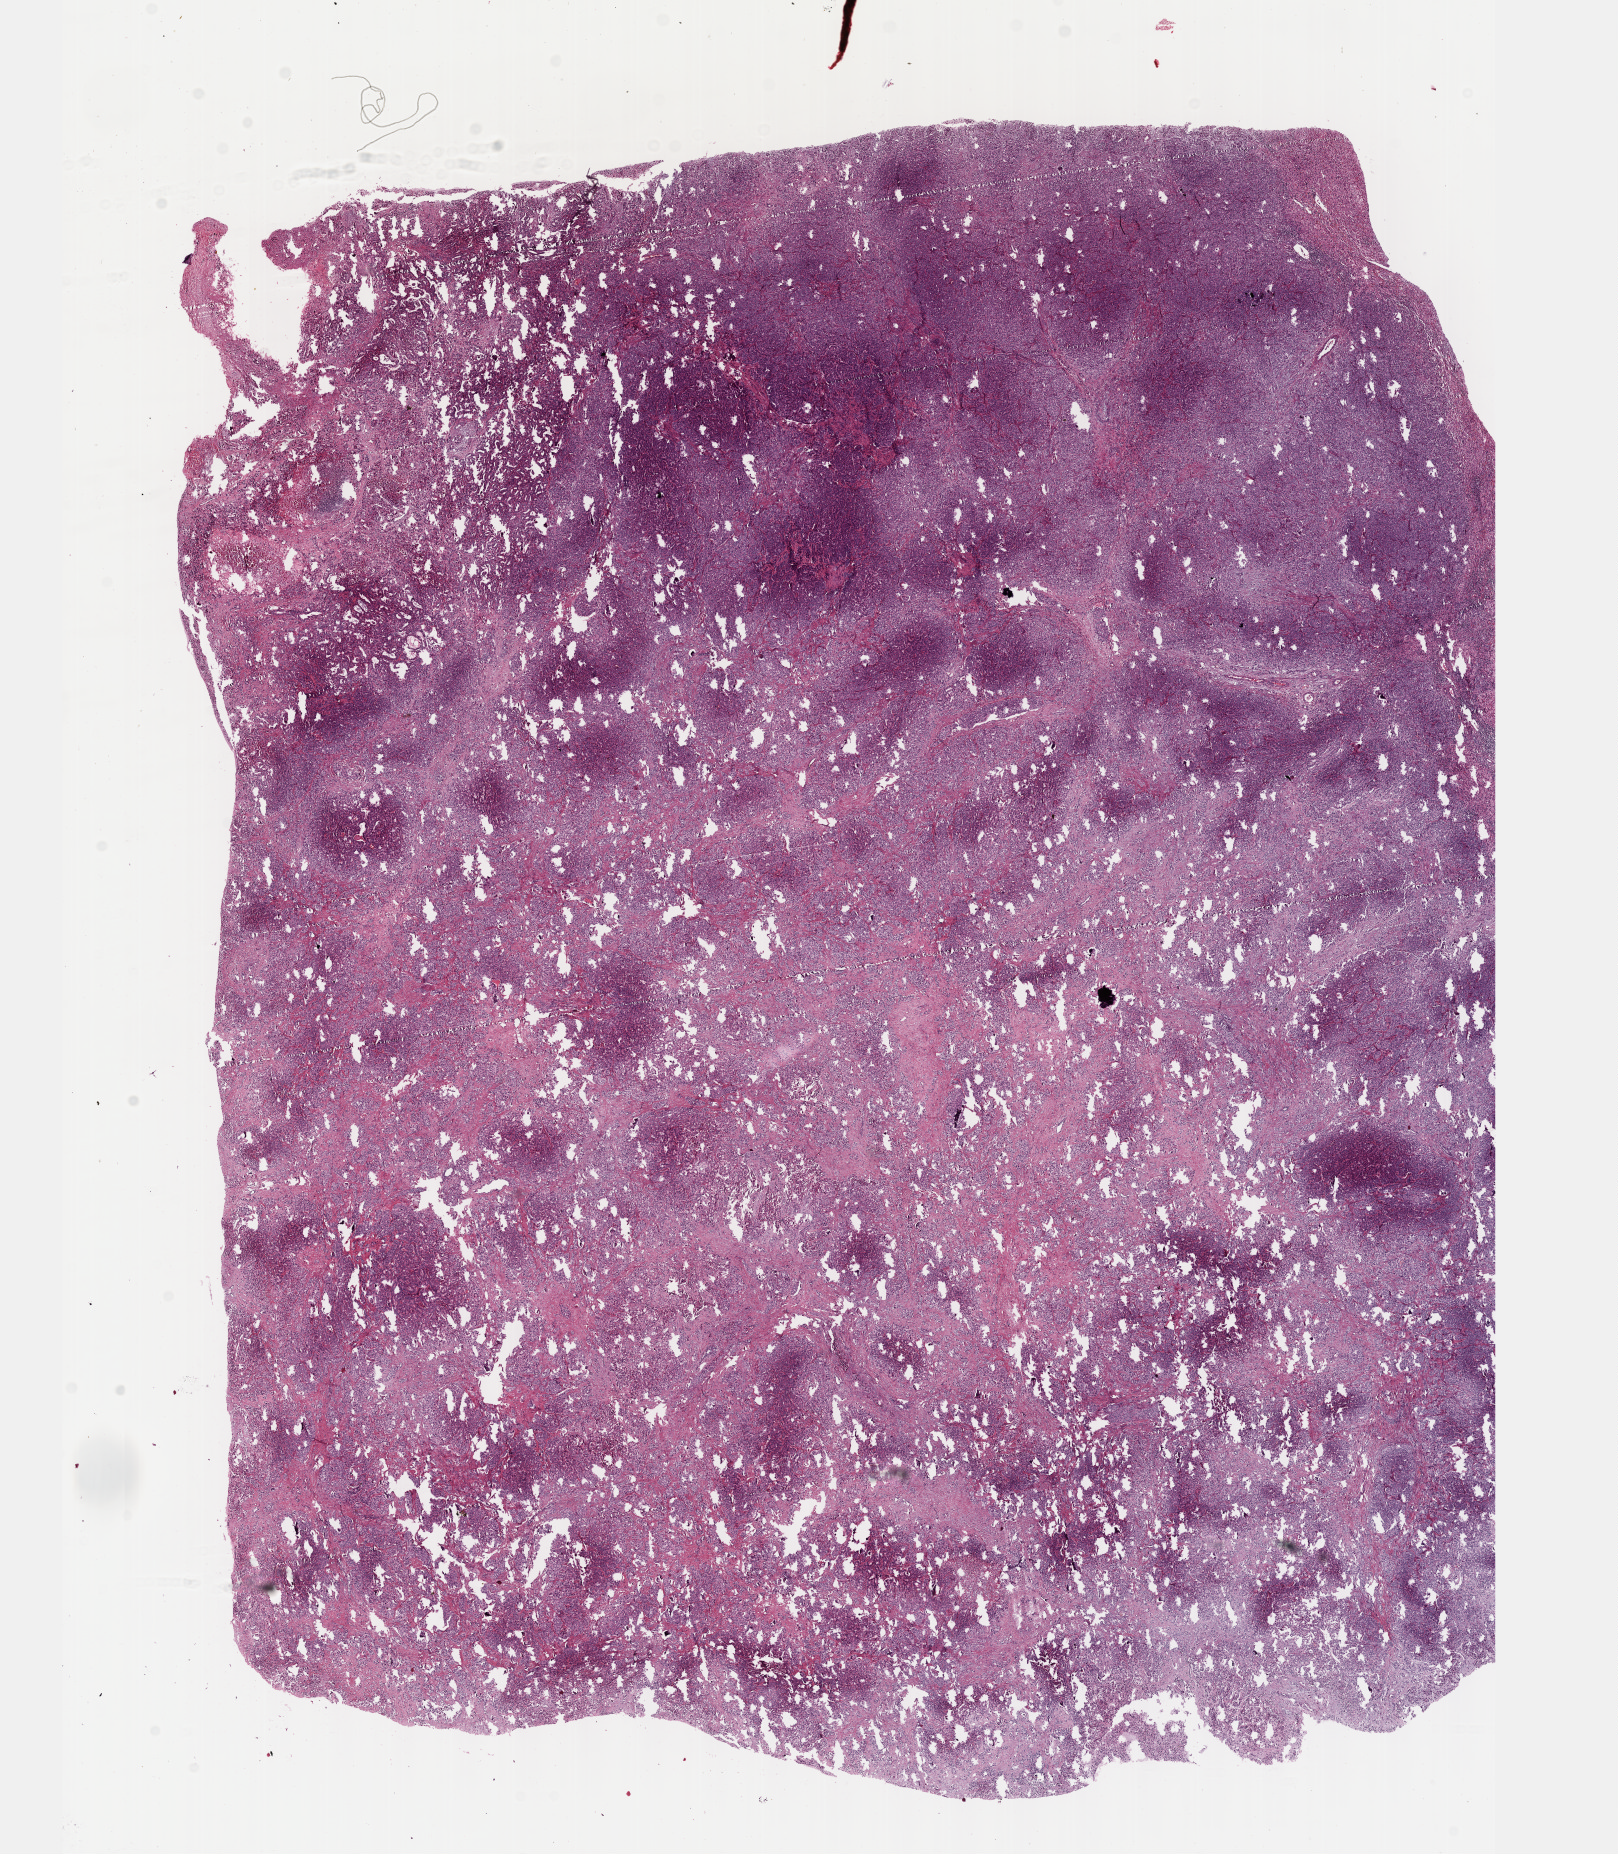
Whole-slide histology image, H&E-stained — shown as a low-resolution overview of the whole scanned area (about 13.1 x 15.0 mm, slide scanned at 40x); formalin-fixed paraffin-embedded (FFPE) diagnostic section; bile duct, primary tumour sample. Patient: female, age at initial diagnosis 73 years. Histologic grade: G3 (poorly differentiated).
AJCC pathologic stage: II (7th edition). Pathologic diagnosis: Cholangiocarcinoma (intrahepatic bile duct).